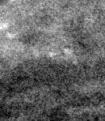
Region of interest cut from a scanned film mammogram (one marked finding), right breast, MLO view, BI-RADS breast density category 1 (scale 1–4).
Finding: calcifications, morphology fine linear branching, distribution clustered / linear; BI-RADS assessment category 5; subtlety rating 4 on a 1 (subtle) to 5 (obvious) scale; pathology result (as recorded, not read from the image): malignant.